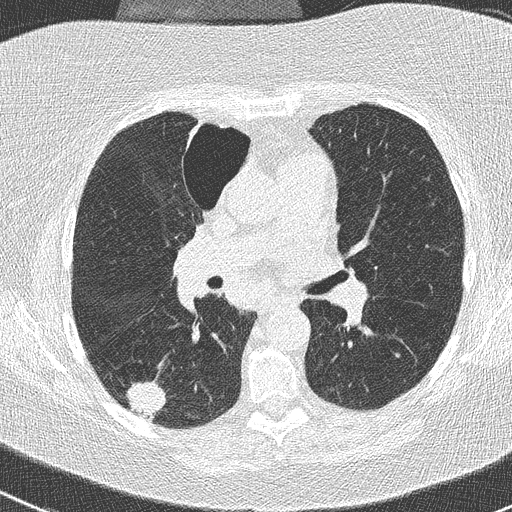
Low-dose screening chest CT, axial slice; baseline screening round; lung window (W 1500 / L -600 HU); 2 mm slice thickness; lung (sharp) reconstruction kernel (B50f); 120 kVp; 512 × 512 image matrix. Female, age 74 years at enrolment. Former smoker at enrolment.
Expert reader's lesion annotation, bounding box [x1, y1, x2, y2] px = [118, 375, 173, 427]. The screening reader recorded 3 non-calcified nodules or masses ≥4 mm on this exam (right lower lobe, right upper lobe, left lower lobe); which of them this box marks is not recorded. Later outcome: lung cancer diagnosed 16 days after this screen — non-small cell carcinoma, right lower lobe, poorly differentiated (G3), stage IIIA (AJCC 6th edition), 28 mm at pathology.